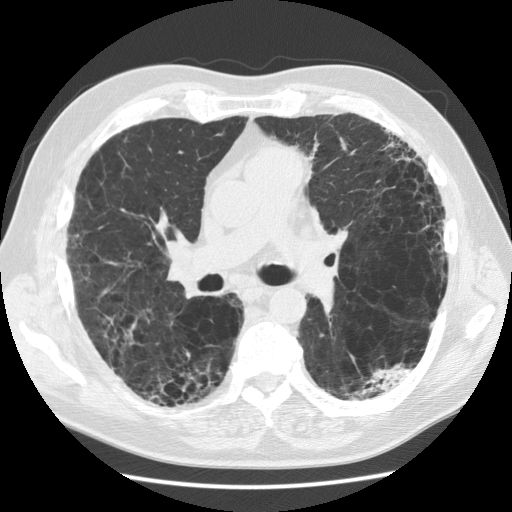
Low-dose screening chest CT, one axial slice. Reconstruction kernel STANDARD. Lung window (W 1500 / L -600 HU). 2.5 mm slice thickness. 512 × 512 image matrix, field of view 360 × 360 mm.
Annotated regions visible in this slice (expert manual segmentation):
- lesion 1 (tumor, lower lobe of left lung): box from (x=367, y=367) to (x=412, y=392) px